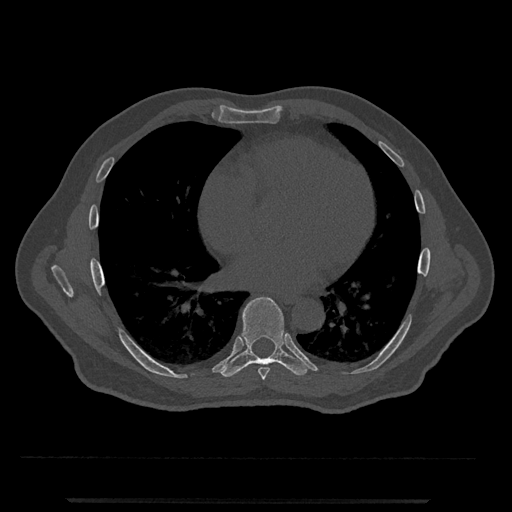
CT including the spine, one axial slice. Reconstruction kernel Br40s/3. 120 kVp. Bone window (W 1800 / L 400 HU). 0.5 mm slice thickness. 512 × 512 image matrix, field of view 419 × 419 mm. Male patient, age 63 years. From the clinical record (not read from this slice): primary cancer: prostate.
Annotated regions visible in this slice (semi-automatic segmentation, software-assisted and operator-edited):
- T7 vertebra: box from (x=258, y=367) to (x=270, y=380) px
- T8 vertebra: (x=222, y=297)–(x=314, y=377)